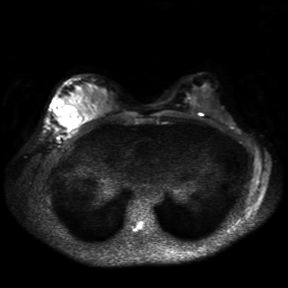
Breast MRI, one axial slice; slice 19 of 30 in the series (ordered by position); diffusion-weighted series; image 2 of 4 stored at this slice position (different b-values; order by instance number); 3 T; 4 mm slice thickness; 288 × 288 image matrix. Female patient.
Structures marked on this image (outlined manually by an expert reader):
- tumour on diffusion-weighted imaging: bounding box (x1, y1, x2, y2) in pixels: (52, 105, 69, 127)